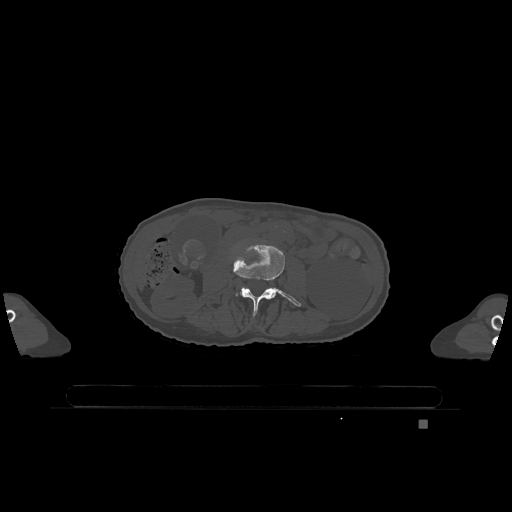
CT including the spine, one axial slice; position 350 of 1317 along the scan axis; bone window (W 1800 / L 400 HU); 0.5 mm slice thickness; 512 × 512 image matrix, field of view 500 × 500 mm. Female patient, age 74 years. Case-level facts recorded for this patient, not image findings: primary cancer: lung.
Annotated regions visible in this slice (semi-automatically segmented with operator editing):
- L3 vertebra: bounding box <233,244,301,316> (left, top, right, bottom; pixels)